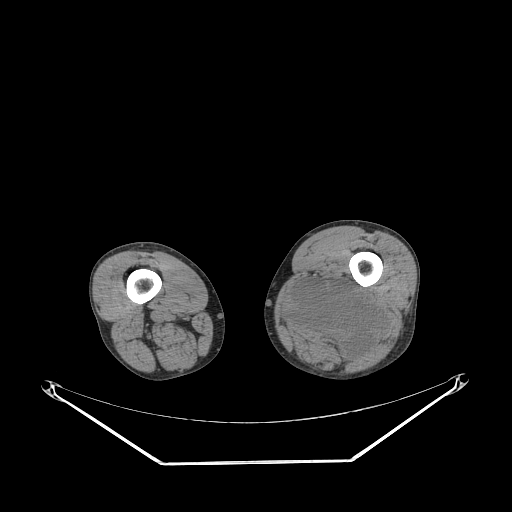
CT of an extremity soft-tissue mass (from a PET/CT study), one axial slice. Position 215 of 267 along the scan axis. Reconstruction kernel STANDARD. Soft-tissue window (W 400 / L 40 HU). 512 × 512 image matrix. Male patient. From the clinical record (not read from this slice): histological type: undifferentiated pleomorphic liposarcoma; grade: high; site of the primary tumour: left thigh.
Annotated regions visible in this slice (expert contour drawn on MRI and transferred to this co-registered scan by the dataset authors):
- gross tumour volume including surrounding oedema: bounding box [x1, y1, x2, y2] px = [285, 272, 382, 359]
- gross tumour volume (mass): [288, 281, 382, 357]